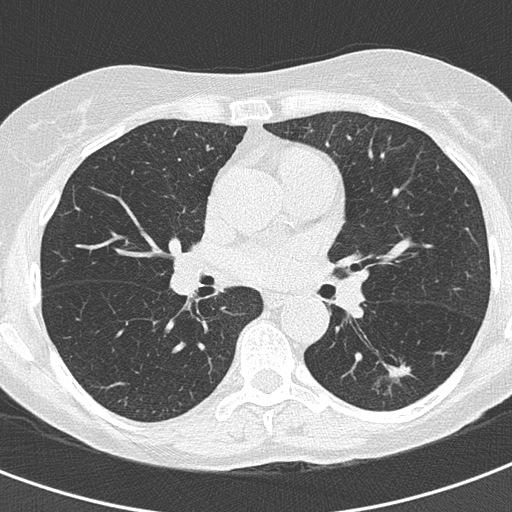
Low-dose screening chest CT, axial slice; second screening round (one year after baseline); lung window (W 1500 / L -600 HU); 2 mm slice thickness; lung (sharp) reconstruction kernel (B50f). Female, age 60 years at enrolment. Current smoker at enrolment.
Lesion marked by an expert reader, bounding box (x1, y1, x2, y2) in pixels: (377, 351, 416, 382). Reader record for this screening exam (exam-level; its link to the box is not recorded): non-calcified nodule or mass ≥4 mm, left lower lobe, 10 × 9 mm, soft tissue attenuation. Participant outcome: lung cancer diagnosed 64 days after this screen — adenocarcinoma, NOS, left lower lobe, well differentiated (G1), stage IA (AJCC 6th edition), 15 mm at pathology.